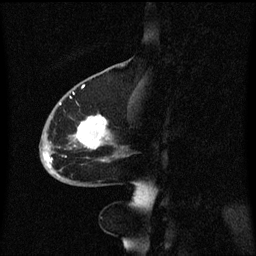
Breast MRI (dynamic contrast-enhanced), one sagittal slice. Slice 24 of 60 in the series (ordered by position). Dynamic contrast-enhanced series, image 2 of 3 at this slice position (ordered by acquisition). 1.5 T. TE 4.2 ms, TR 8.4 ms. 2 mm slice thickness. 256 × 256 image matrix, field of view 200 × 200 mm. Patient: female, 68 years. From the clinical record (not read from this slice): setting: breast cancer imaged before/during neoadjuvant chemotherapy; receptor status: triple-negative.
Outlined on this slice (semi-automatic segmentation, software-assisted and operator-edited):
- analysis volume of interest (the breast-tissue region the enhancement analysis was run in; not a lesion): bounding box <40,94,128,173> (left, top, right, bottom; pixels)
- tumour enhancement mask (voxels above the 70 % enhancement threshold inside the analysis volume of interest): <44,104,111,169>